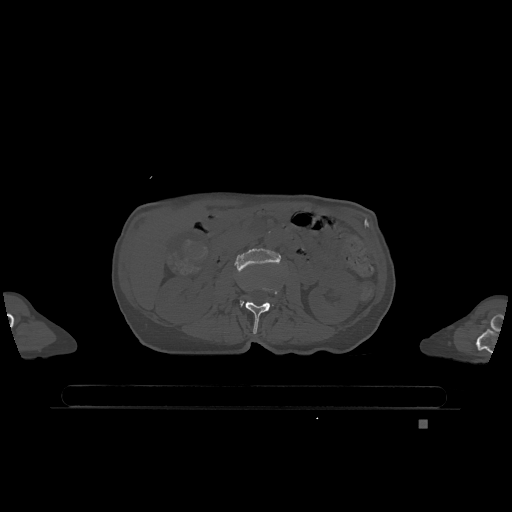
CT including the spine, one axial slice. Position 397 of 1317 along the scan axis. Bone window (W 1800 / L 400 HU). 0.5 mm slice thickness. 512 × 512 image matrix. Patient: female, 74 years. From the clinical record (not read from this slice): primary cancer: lung; vertebrae with lytic lesions (as recorded): T1, T4, T5, T6, L4, L5.
Outlined on this slice (semi-automatic segmentation, software-assisted and operator-edited):
- L2 vertebra: bounding box <245,287,279,334> (left, top, right, bottom; pixels)
- L3 vertebra: <235,248,281,305>